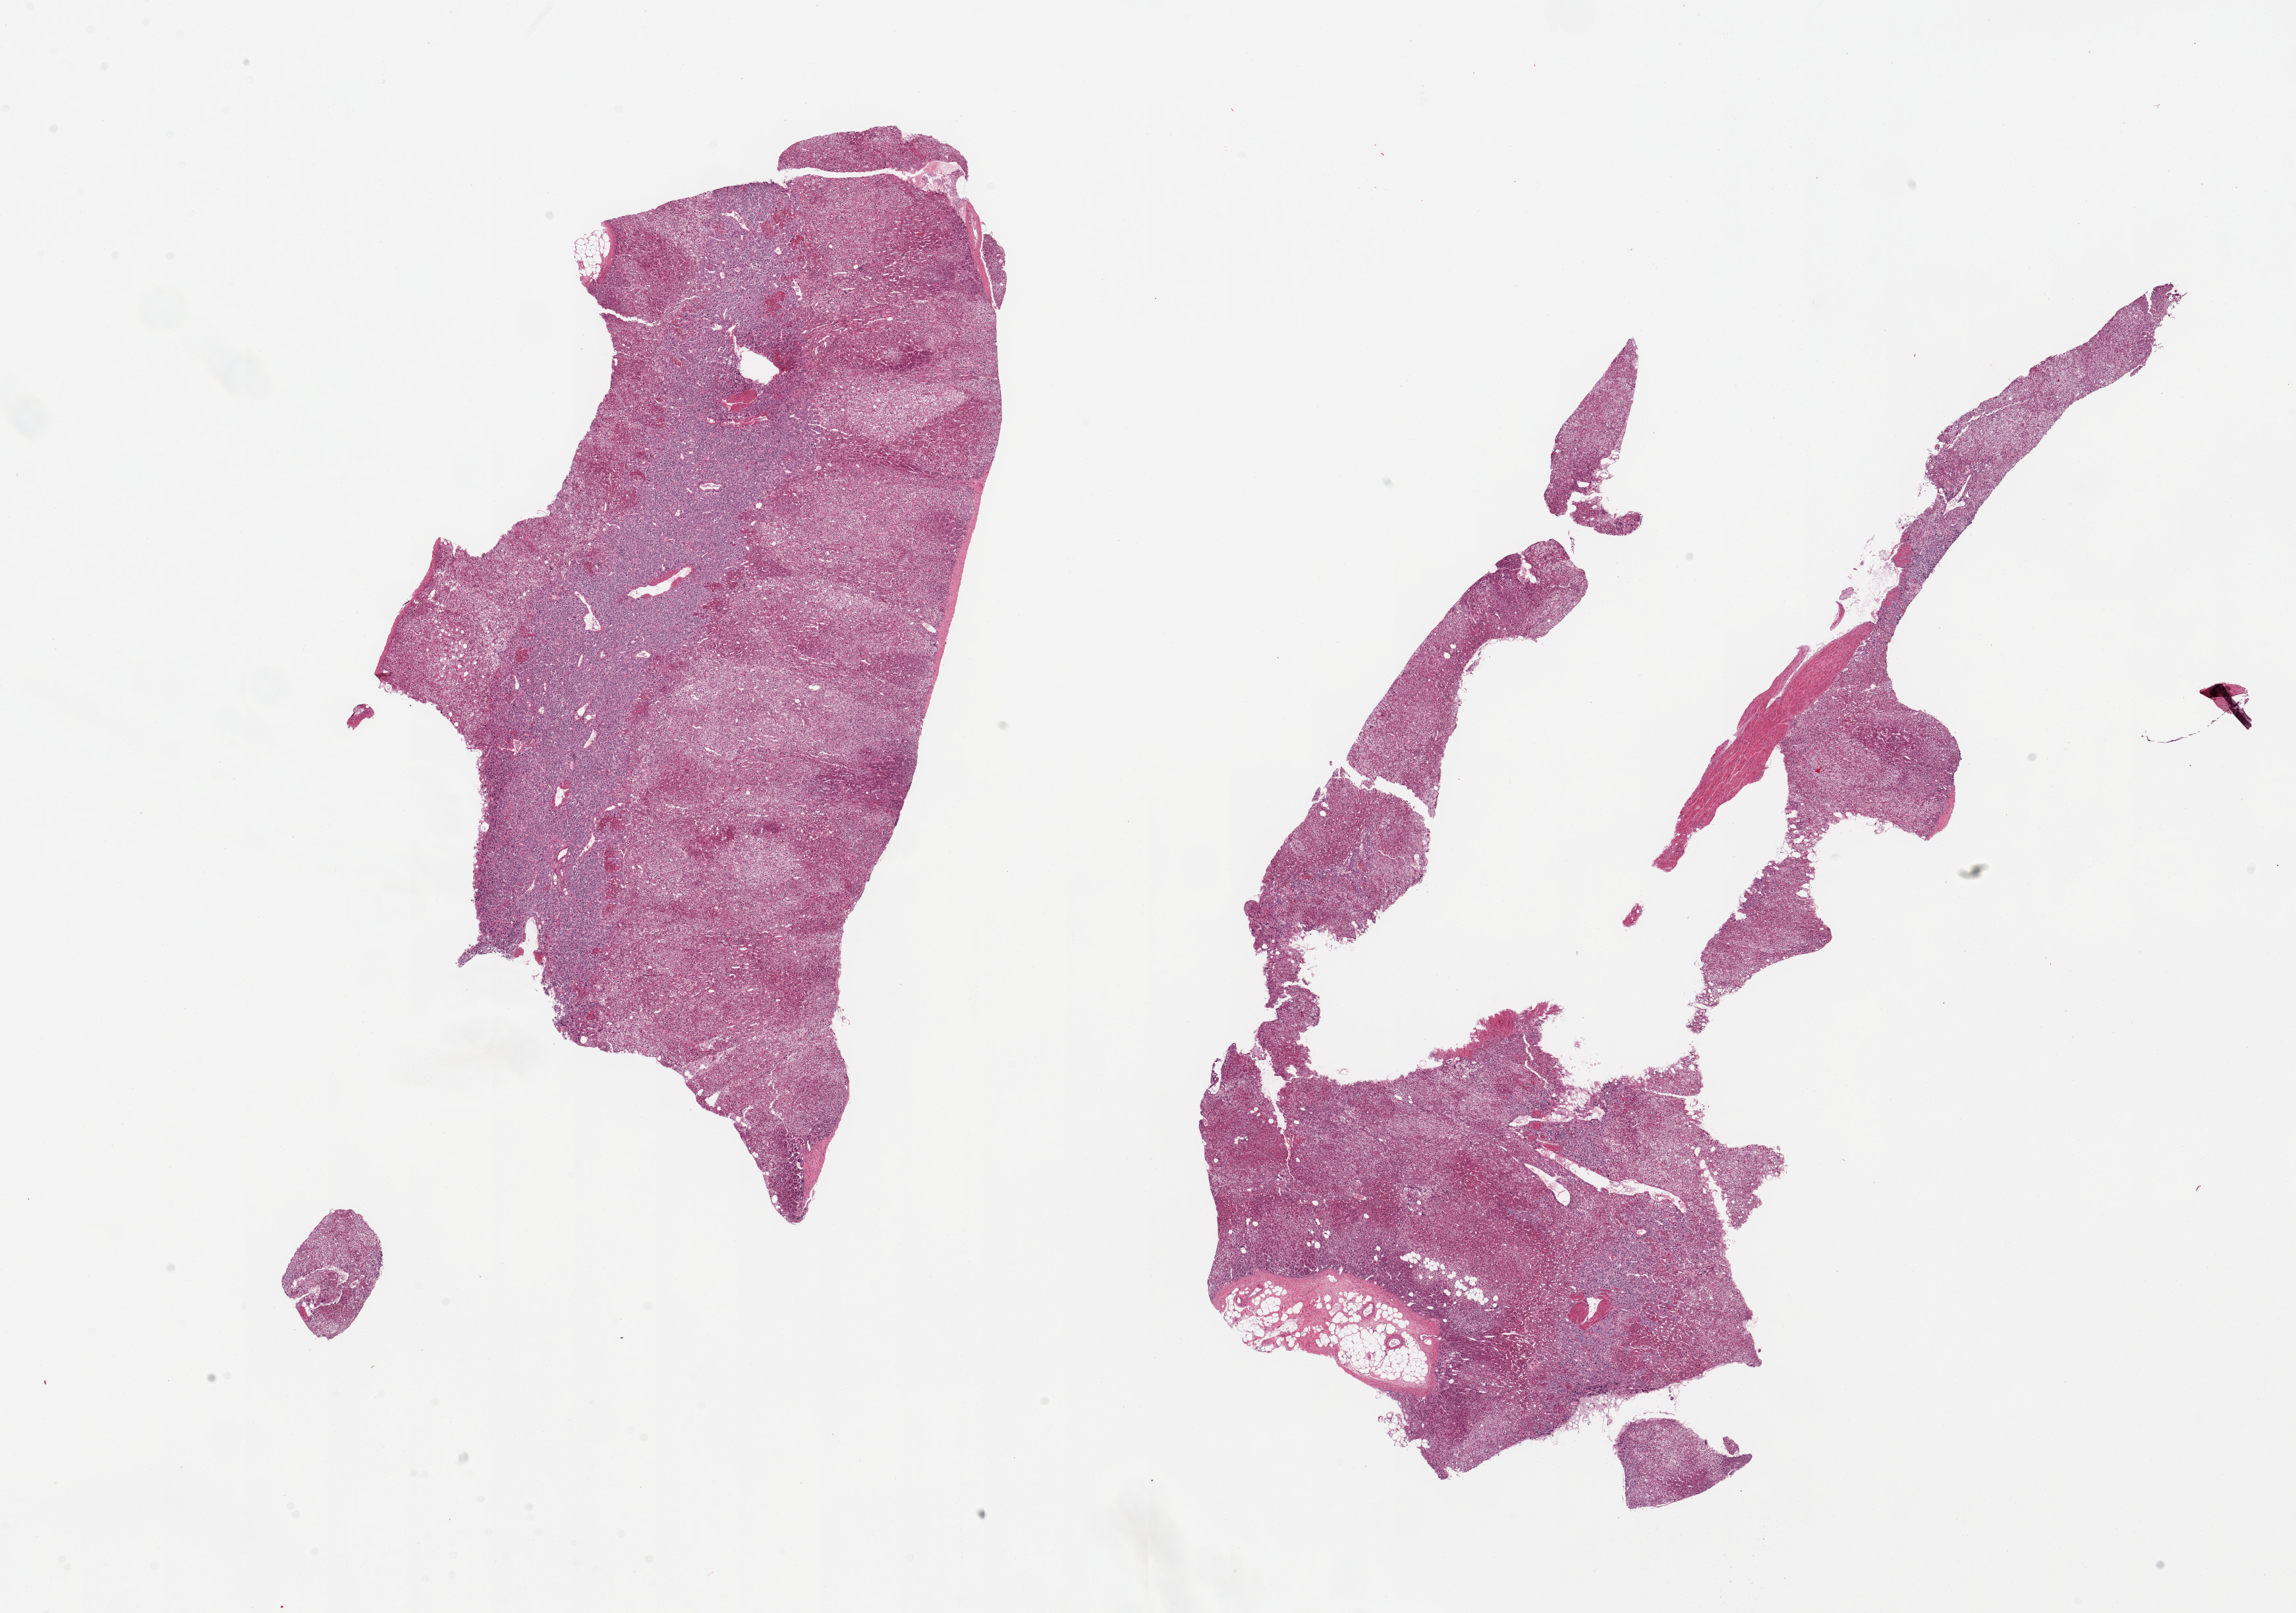
Haematoxylin and eosin whole-slide image, brightfield, shown as a low-resolution overview of the whole scanned area (about 27.6 x 19.4 mm, acquisition: 20x scan). PAXgene-fixed, paraffin-embedded tissue. Sampled site (target tissue): adrenal gland. Donor tissue sample. Male donor.
Pathologist's review note for this sample: 2 pieces; cortex and medulla, small amount of external fat attached to one piece.